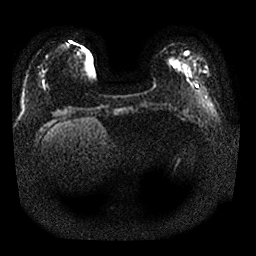
Breast MRI, one axial slice; position 4 of 25 along the scan axis; diffusion-weighted series; image 2 of 4 stored at this slice position (different b-values; order by instance number); 1.5 T; 4 mm slice thickness; 256 × 256 image matrix. Female patient.
Annotated regions visible in this slice (manually delineated by an expert):
- tumour on diffusion-weighted imaging: bounding box [x1, y1, x2, y2] px = [172, 59, 182, 67]